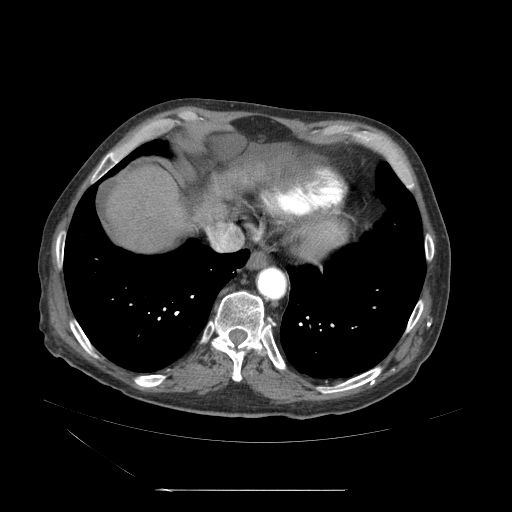
Contrast-enhanced abdominal CT (liver protocol), one axial slice. Slice 55 of 71 in the series (ordered by position). Reconstruction kernel STANDARD. Soft-tissue window (W 400 / L 40 HU). 2.5 mm slice thickness. 512 × 512 image matrix. From the clinical record (not read from this slice): diagnosis: hepatocellular carcinoma (patient treated with transarterial chemoembolisation; whether this scan precedes or follows treatment is not stated here); TNM stage (as recorded): Stage-II; Child-Pugh class: A; tumour nodularity: multinodular.
Structures marked on this image (semi-automatic segmentation, software-assisted and operator-edited):
- abdominal aorta: bounding box [x1, y1, x2, y2] px = [257, 268, 287, 301]
- liver parenchyma outside the tumour (the mass and vessels are separate outlines, so this box may not span the whole liver): [116, 148, 309, 252]
- liver vessels: [213, 225, 246, 253]